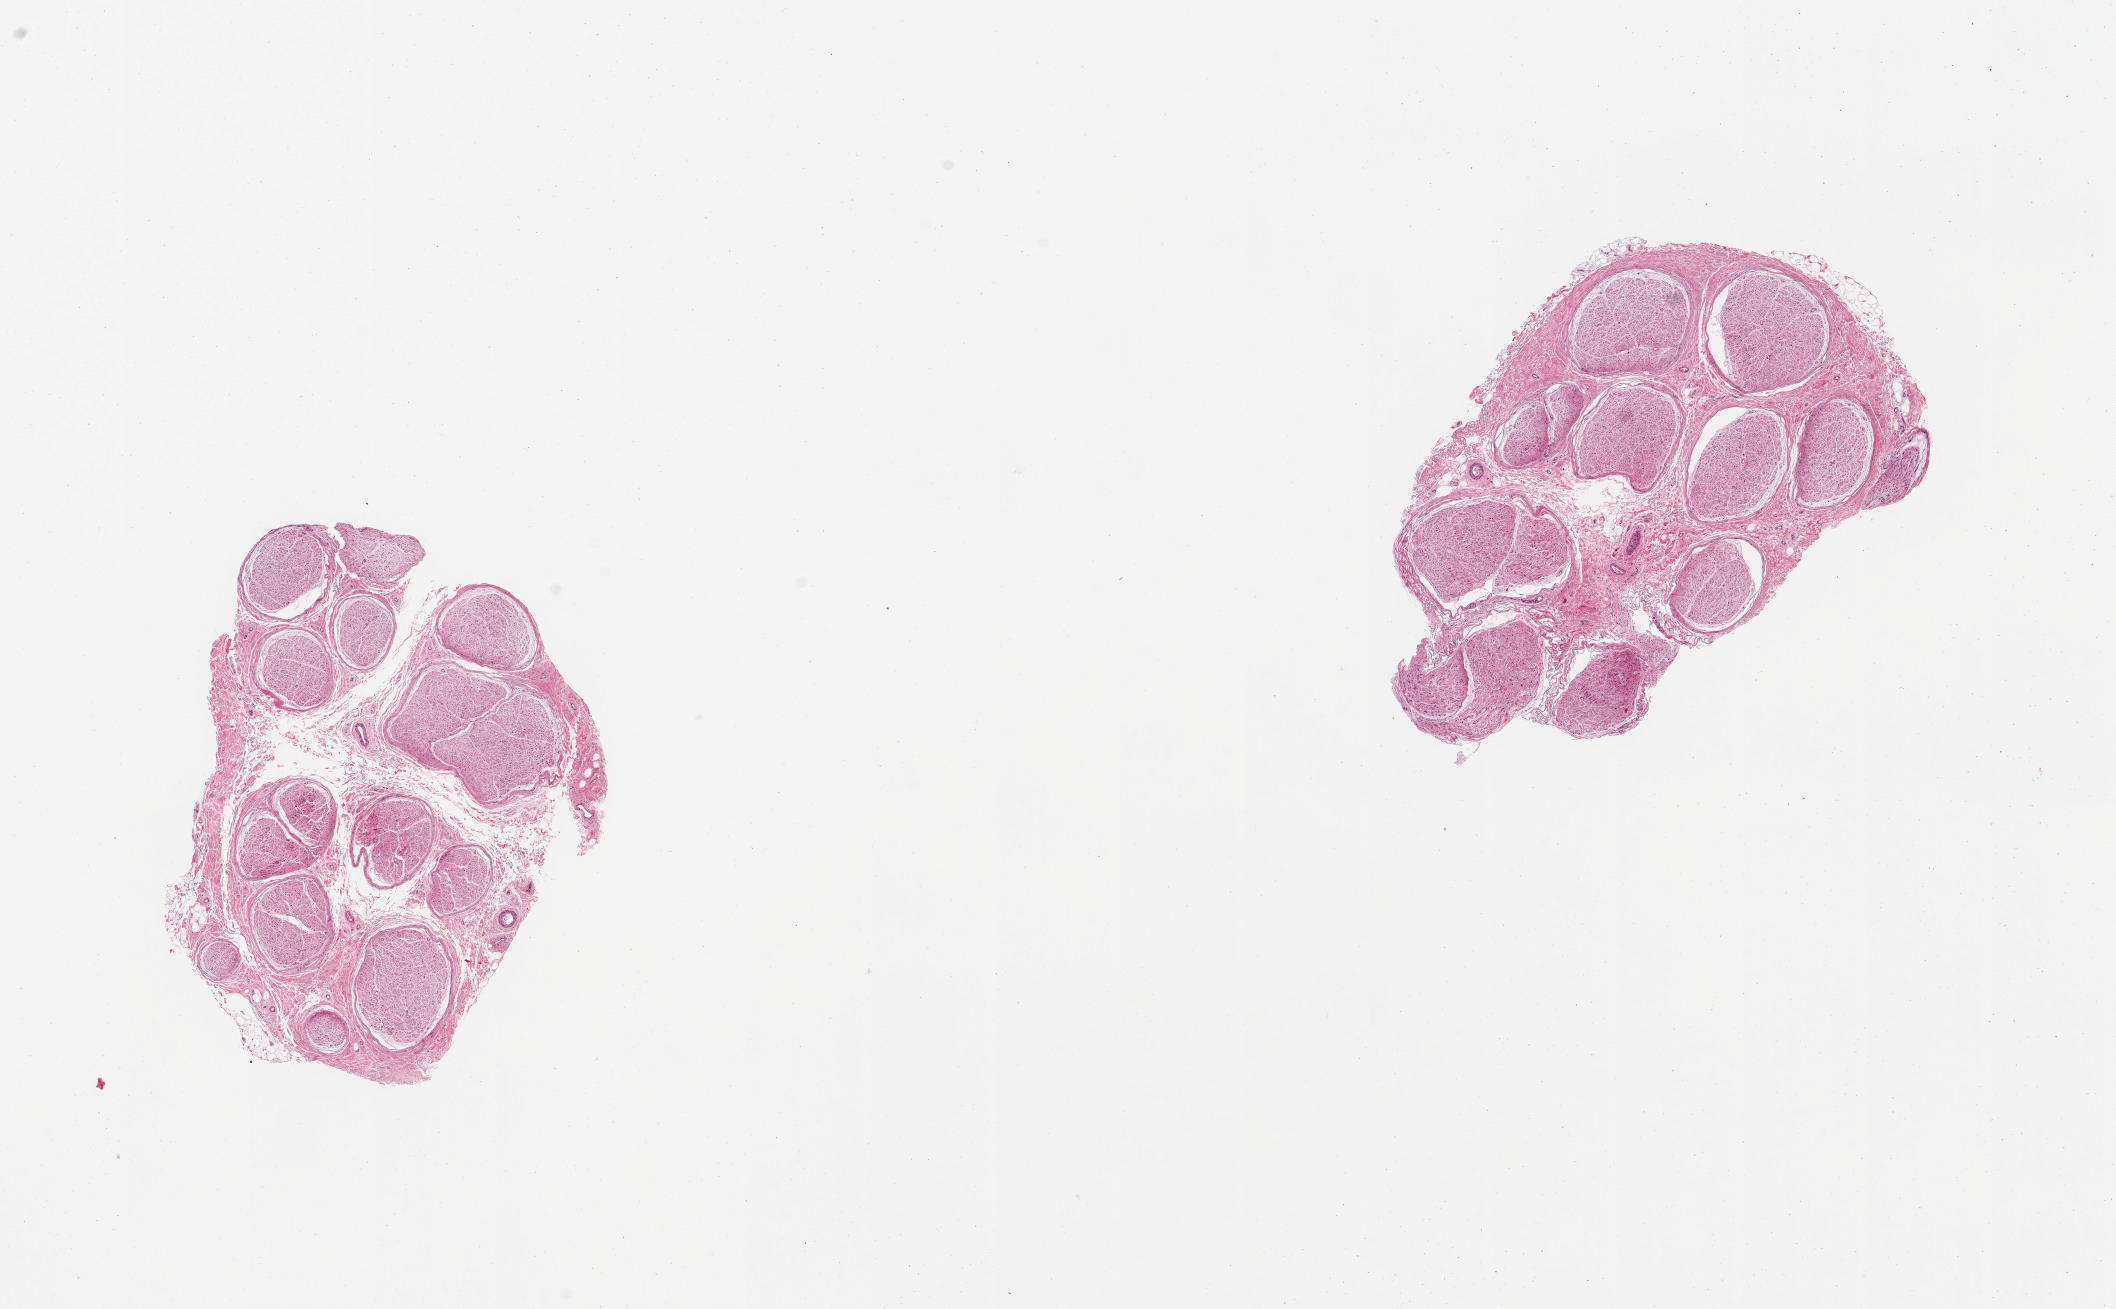
Hematoxylin and eosin (H&E) whole-slide image, shown as a low-resolution overview of the whole scanned area (about 16.7 x 10.4 mm, from a 20x scan). PAXgene-fixed, paraffin-embedded tissue. Sampled site (target tissue): tibial nerve. Donor tissue sample. Donor sex: male.
Pathologist's review note for this sample: 2 pieces; 5% attached fat.